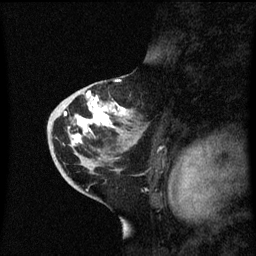
Breast MRI (dynamic contrast-enhanced), one sagittal slice. Slice 35 of 60 in the series (ordered by position). Dynamic contrast-enhanced series, image 2 of 3 at this slice position (ordered by acquisition). 1.5 T. TE 4.2 ms, TR 8.4 ms. 2.3 mm slice thickness. 256 × 256 image matrix, field of view 200 × 200 mm. Female patient, age 46 years. Case-level facts recorded for this patient, not image findings: setting: breast cancer imaged before/during neoadjuvant chemotherapy; receptor status: HER2-positive.
Structures marked on this image (semi-automatic segmentation, software-assisted and operator-edited):
- analysis volume of interest (the breast-tissue region the enhancement analysis was run in; not a lesion): bounding box (x1, y1, x2, y2) in pixels: (48, 86, 145, 171)
- tumour enhancement mask (voxels above the 70 % enhancement threshold inside the analysis volume of interest): (64, 92, 127, 147)